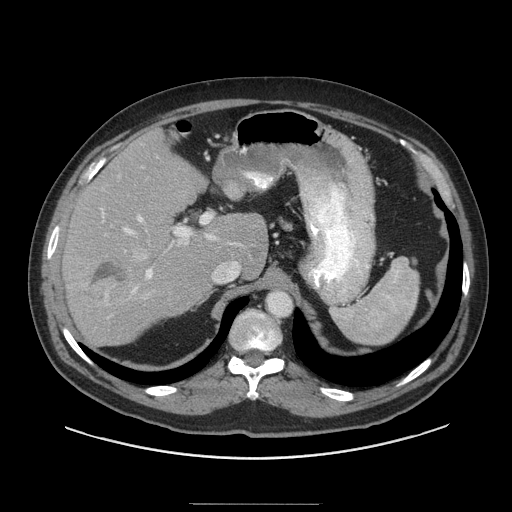
Contrast-enhanced abdominal CT (liver protocol), one axial slice. Position 65 of 91 along the scan axis. Reconstruction kernel STANDARD. Soft-tissue window (W 400 / L 40 HU). 2.5 mm slice thickness. 512 × 512 image matrix. From the clinical record (not read from this slice): diagnosis: hepatocellular carcinoma (patient treated with transarterial chemoembolisation; whether this scan precedes or follows treatment is not stated here); TNM stage (as recorded): Stage-I.
Annotated regions visible in this slice (semi-automatic segmentation, software-assisted and operator-edited):
- liver parenchyma outside the tumour (the mass and vessels are separate outlines, so this box may not span the whole liver): box from (x=62, y=130) to (x=266, y=346) px
- mass: (x=85, y=256)–(x=138, y=303)
- liver vessels: (x=101, y=209)–(x=237, y=293)